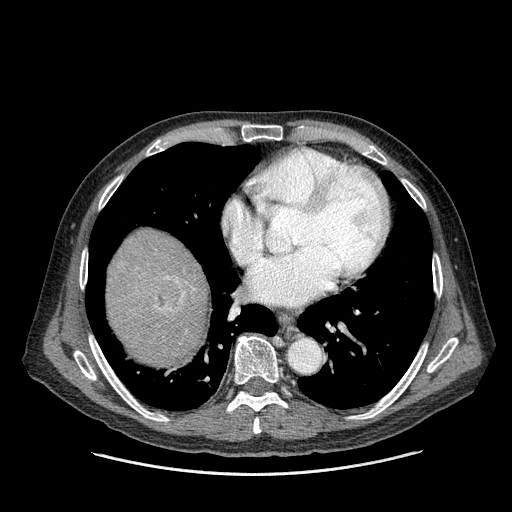
Contrast-enhanced abdominal CT (liver protocol), one axial slice. Position 152 of 180 along the scan axis. Reconstruction kernel STANDARD. One of 2 acquisitions stored at this slice position. Soft-tissue window (W 400 / L 40 HU). 2.5 mm slice thickness. 512 × 512 image matrix, field of view 420 × 420 mm. Case-level facts recorded for this patient, not image findings: diagnosis: hepatocellular carcinoma (patient treated with transarterial chemoembolisation; whether this scan precedes or follows treatment is not stated here); TNM stage (as recorded): Stage-II; Child-Pugh class: A; tumour differentiation: well differentiated; tumour nodularity: multinodular.
Outlined on this slice (semi-automatically segmented with operator editing):
- liver parenchyma outside the tumour (the mass and vessels are separate outlines, so this box may not span the whole liver): bounding box <106,228,208,364> (left, top, right, bottom; pixels)
- mass: <146,274,187,314>
- liver vessels: <193,288,195,290>